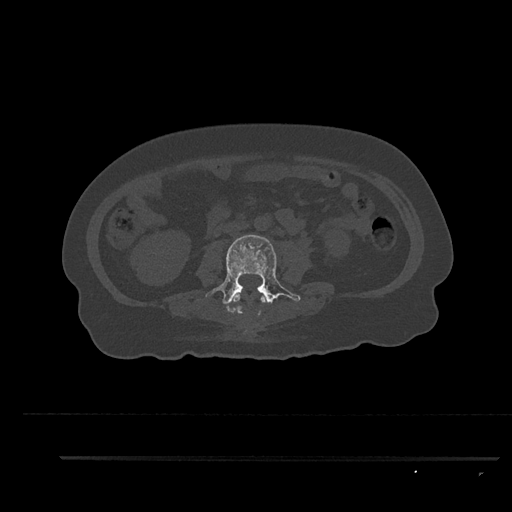
CT including the spine, one axial slice. Position 100 of 797 along the scan axis. Reconstruction kernel Br40s/3. 120 kVp. Bone window (W 1800 / L 400 HU). 0.5 mm slice thickness. 512 × 512 image matrix. Patient: female, 44 years. Case-level facts recorded for this patient, not image findings: primary cancer: renal; vertebrae with lytic lesions (as recorded): L1.
Outlined on this slice (semi-automatic segmentation, software-assisted and operator-edited):
- L2 vertebra: bounding box (x1, y1, x2, y2) in pixels: (230, 294, 265, 315)
- L3 vertebra: (206, 235, 300, 314)